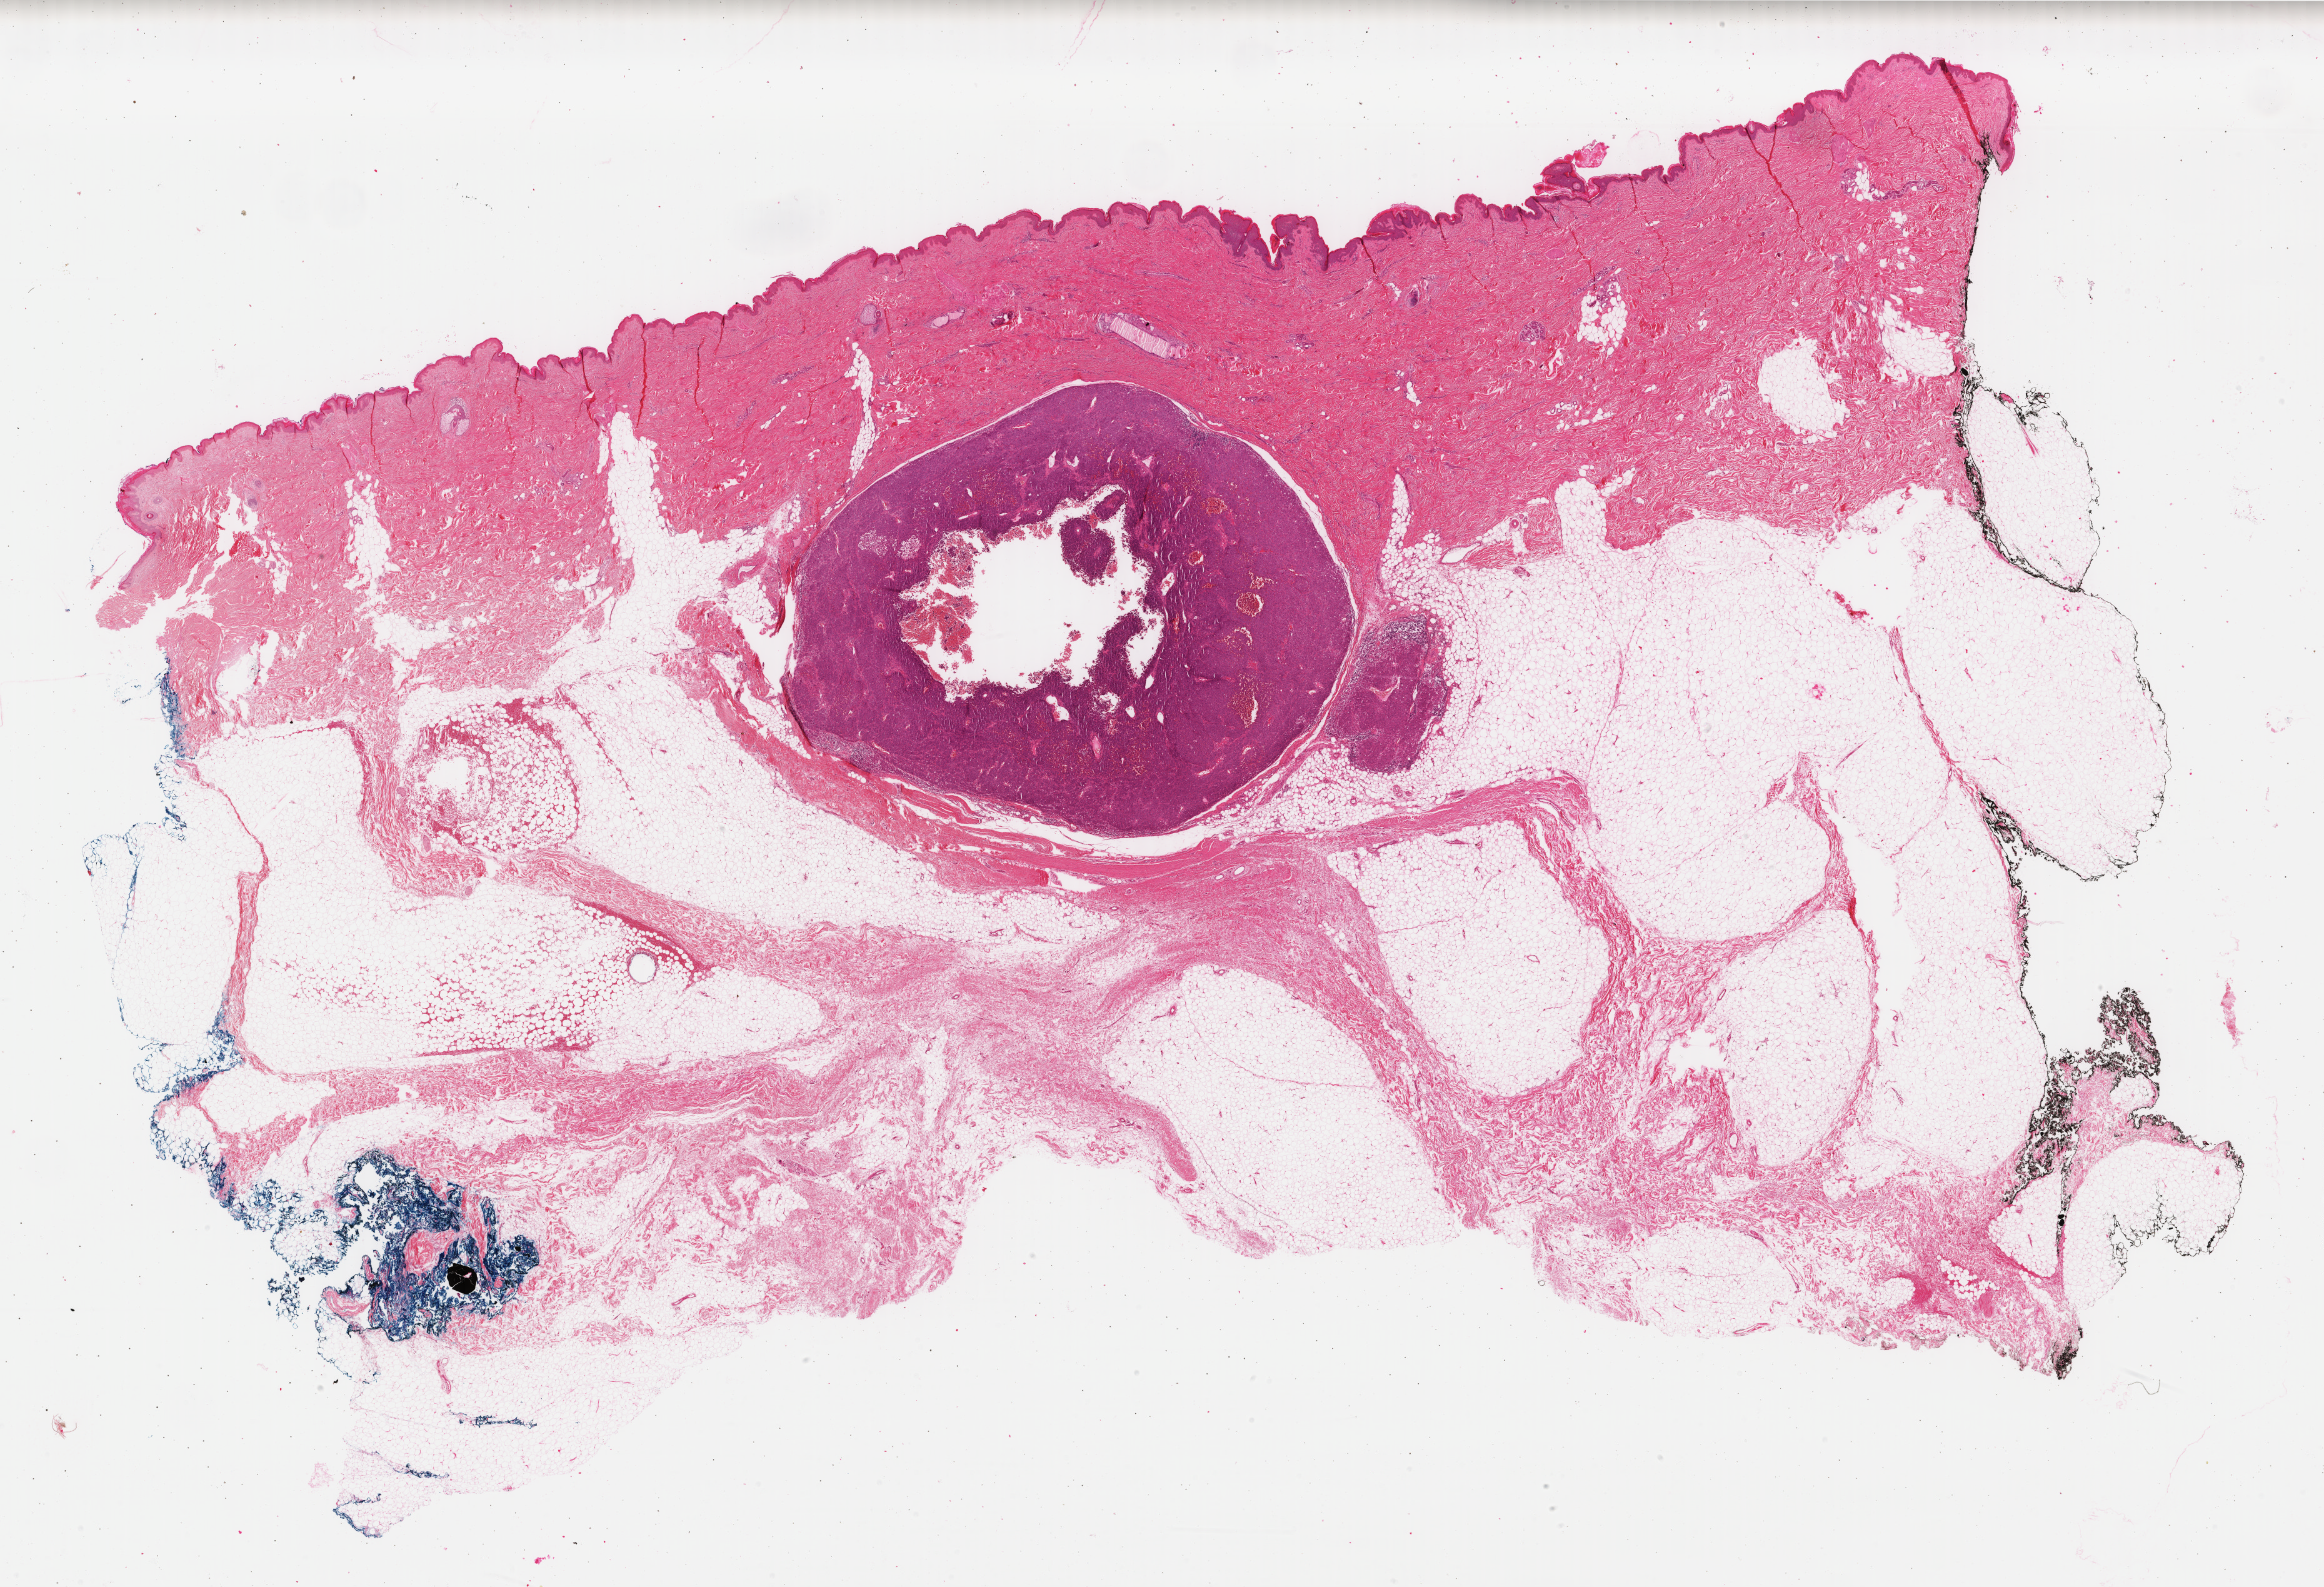
H&E-stained whole-slide image, whole scanned area (about 29.5 x 20.2 mm, acquisition: 40x scan) shown as a low-resolution overview, formalin-fixed paraffin-embedded (FFPE) diagnostic section, primary tumour sample from the skin. Patient: female, age at initial diagnosis 70 years.
Diagnosis: Malignant melanoma, NOS.